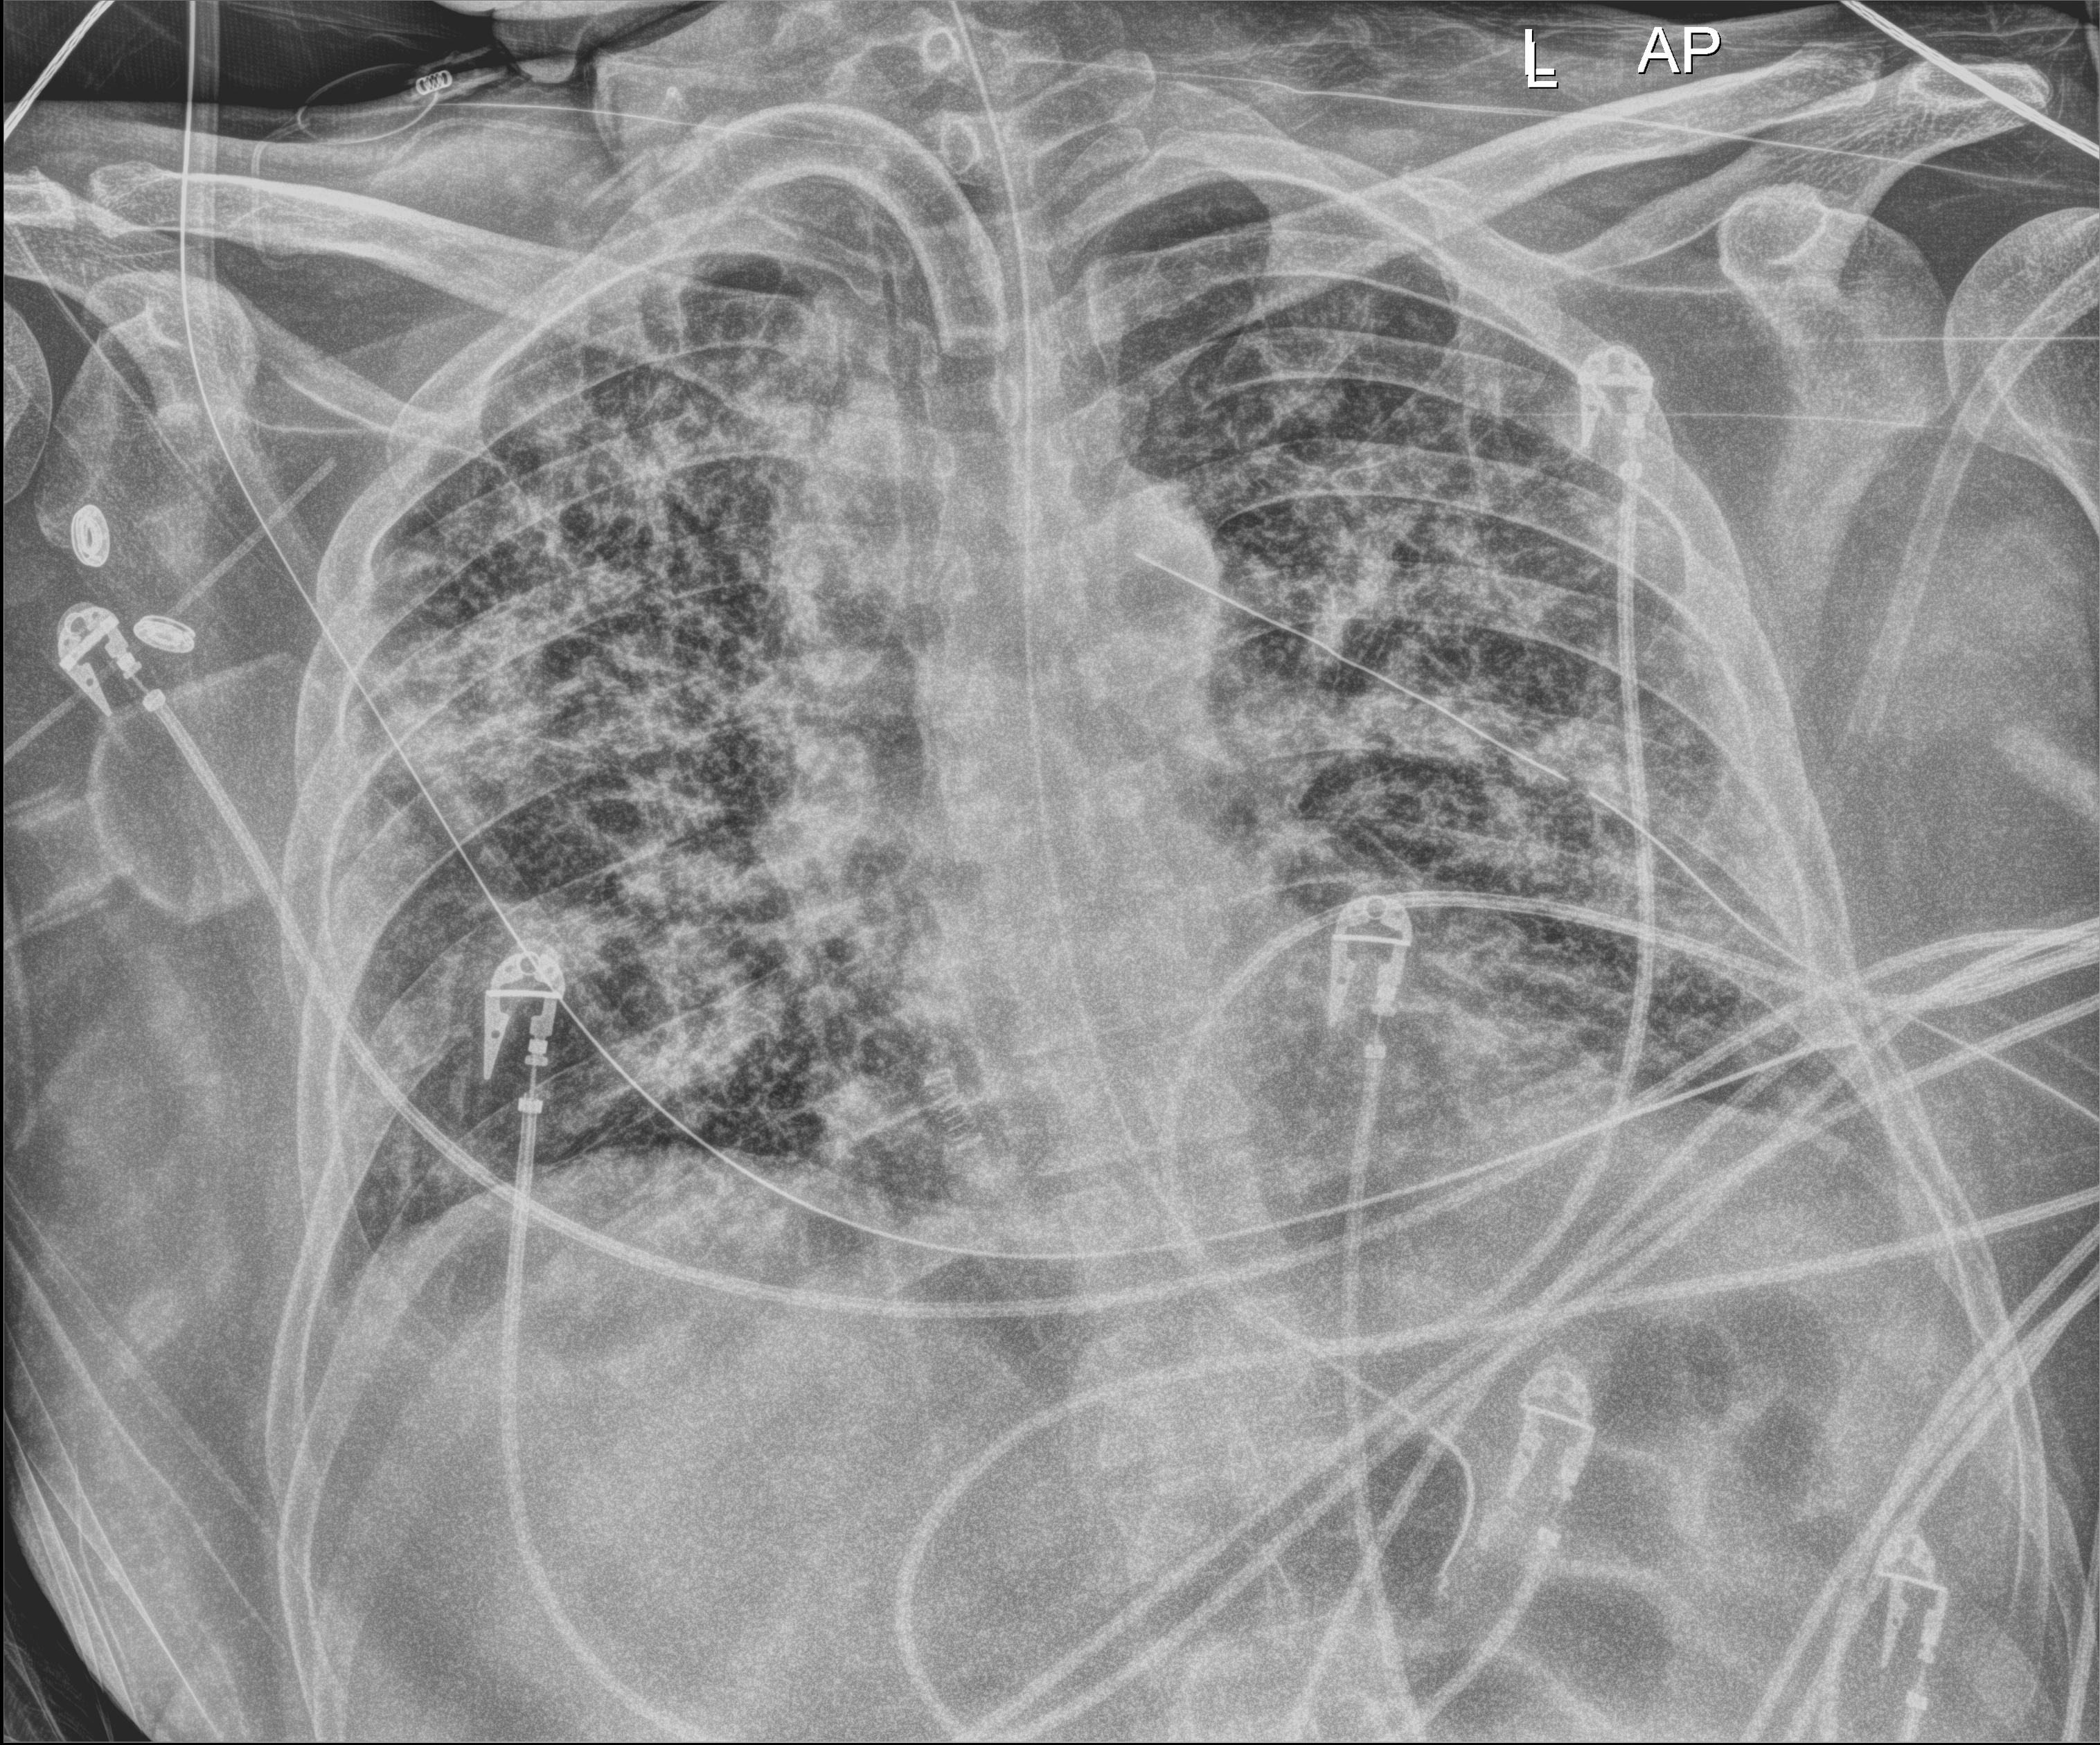
Chest X-ray; anteroposterior (AP) projection. Patient hospitalised with COVID-19; male, aged 18–59 years.
Hospital-stay facts (about this admission, not read from this image; timing relative to this image not recorded): admitted to intensive care during this hospital stay: yes; chronic kidney disease (admission record): no; mechanically ventilated during this hospital stay: yes.